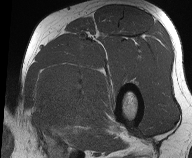
MRI of an extremity soft-tissue mass, one axial slice; slice 42 of 61 in the series (ordered by position); MR volume resampled by the dataset authors to the PET/CT grid (not the native acquisition matrix); 192 × 158 image matrix. Male patient. Case-level facts recorded for this patient, not image findings: histological type: pleiomorphic liposarcoma; grade: high; site of the primary tumour: left thigh.
Structures marked on this image (expert contour drawn on MRI and transferred to this co-registered scan by the dataset authors):
- gross tumour volume including surrounding oedema: bounding box <32,69,92,133> (left, top, right, bottom; pixels)
- gross tumour volume (mass): <36,73,83,113>